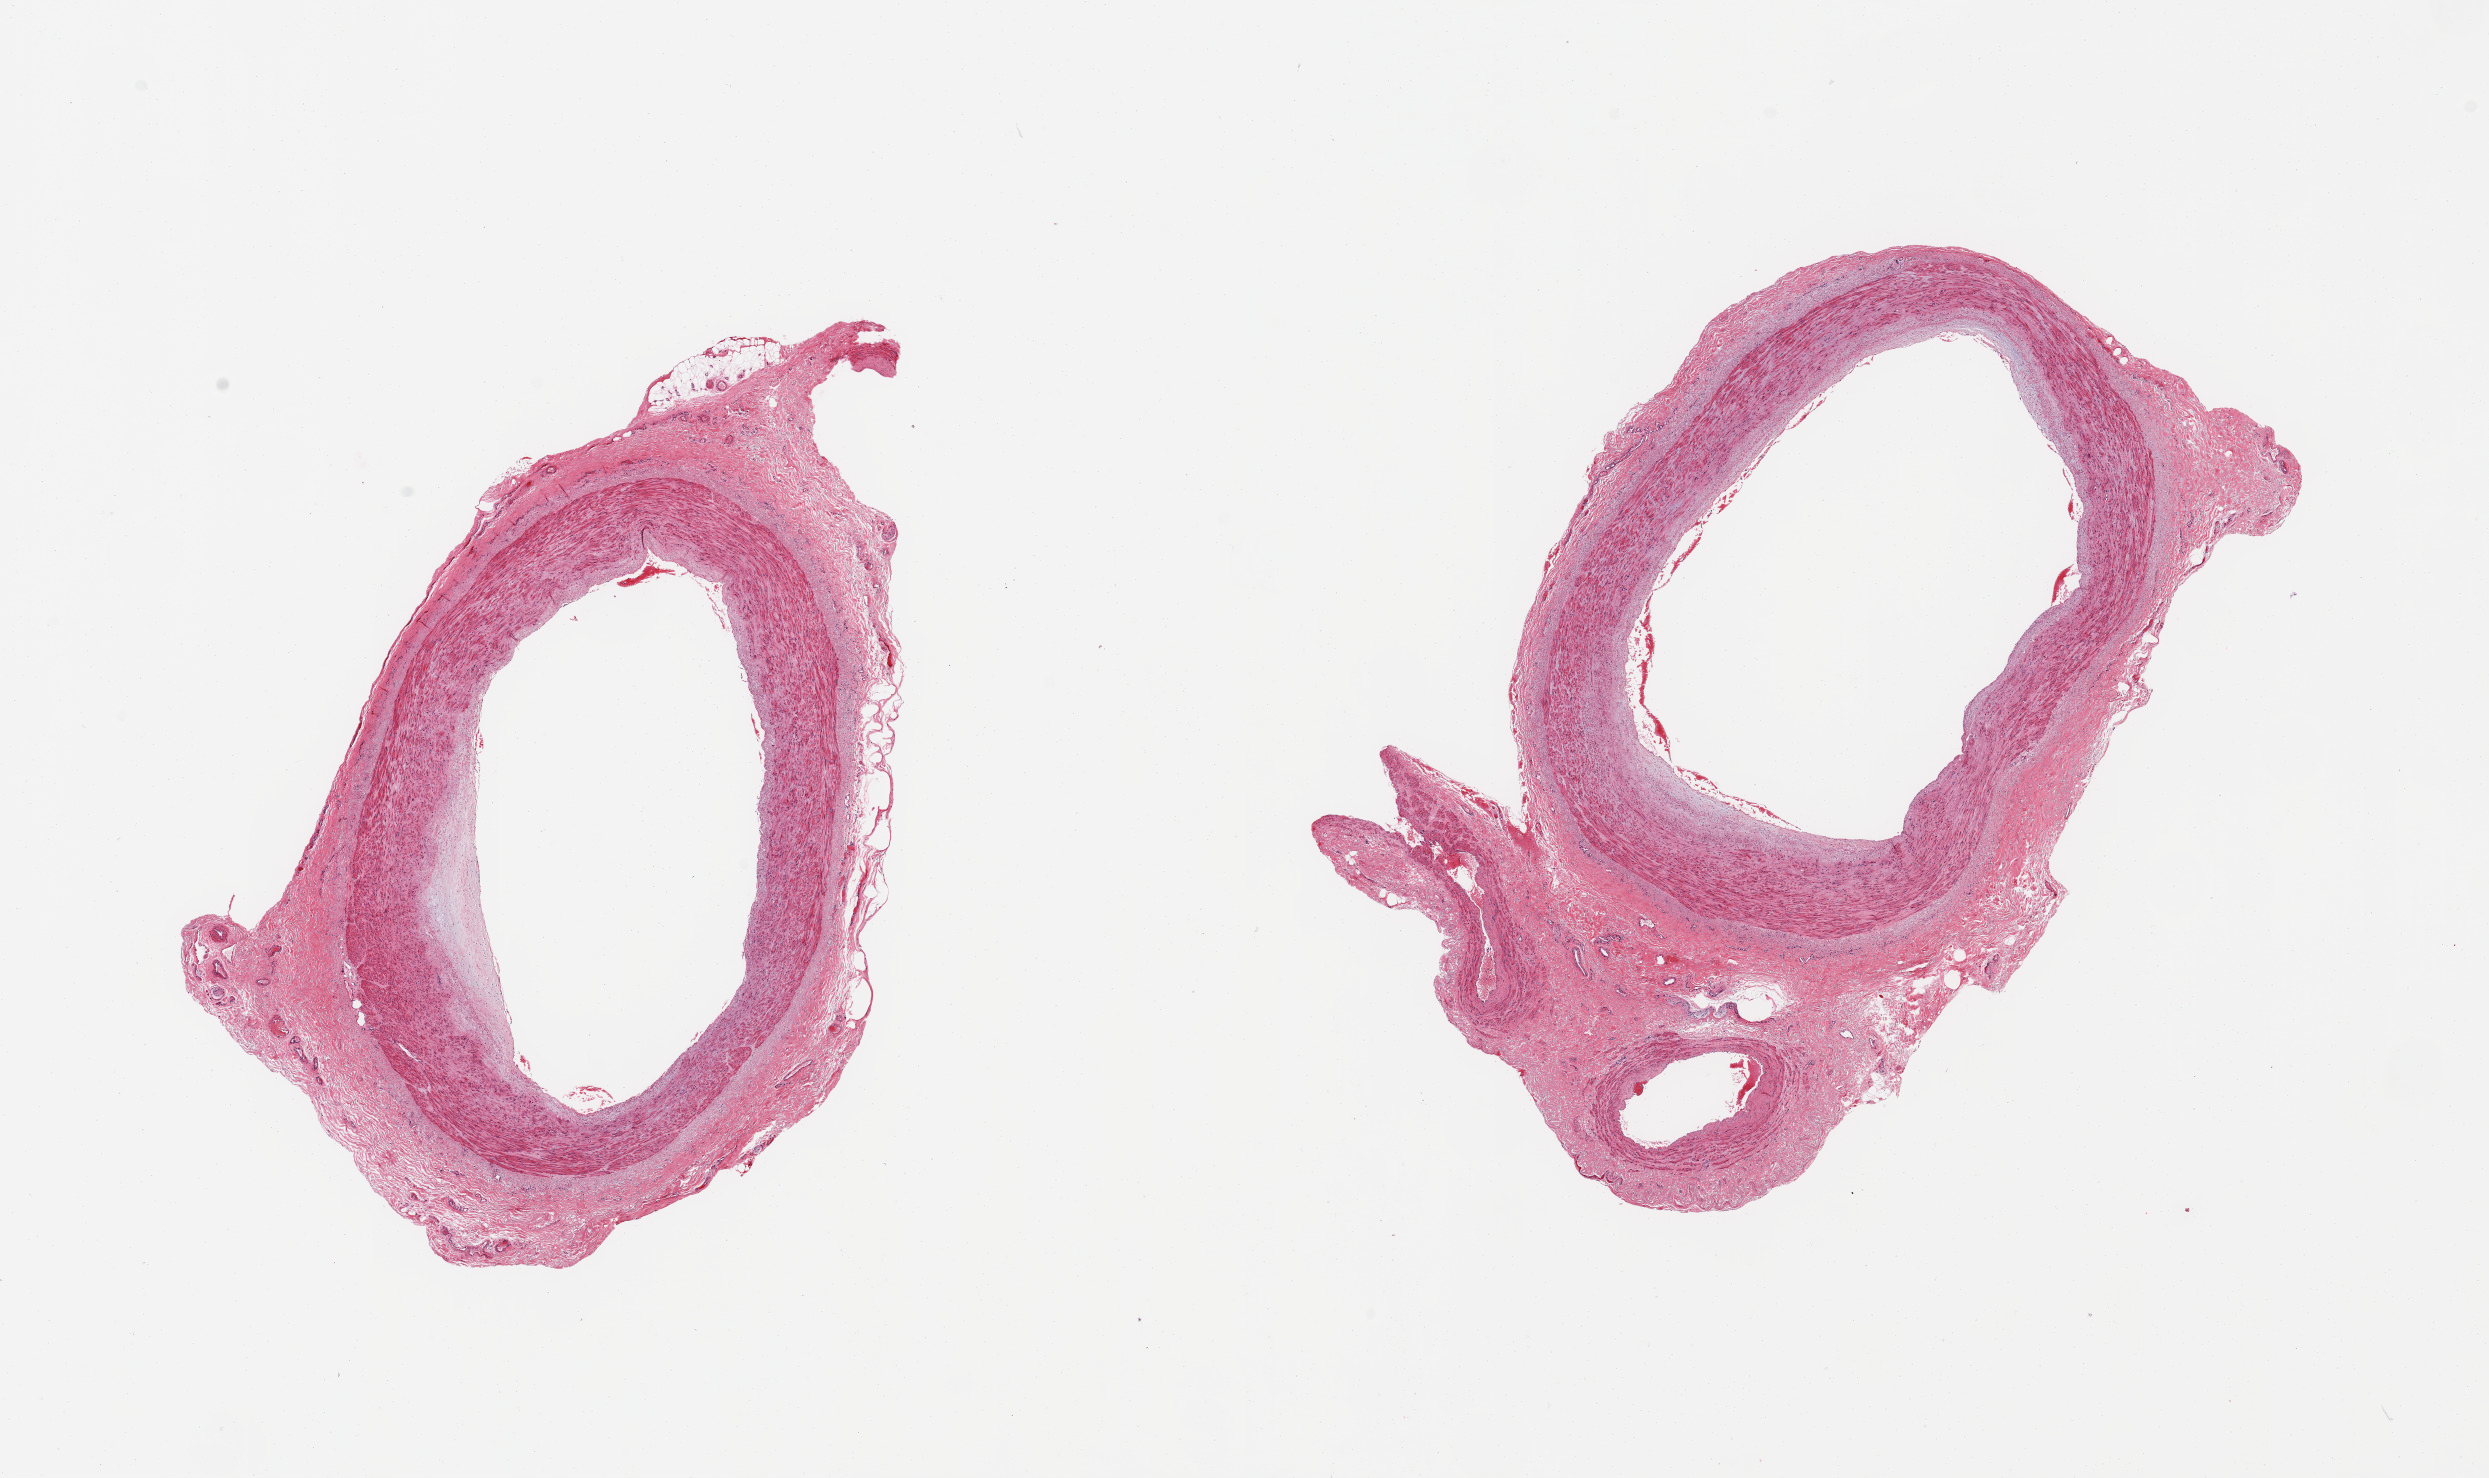
Whole-slide image, haematoxylin and eosin stain, brightfield, low-resolution overview of the scanned area, about 19.7 x 11.7 mm (slide scanned at 20x), PAXgene-fixed, paraffin-embedded tissue, target tissue: tibial artery, donor tissue sample. Donor sex: male.
Reviewer comment on this tissue sample: 2 pieces; small attachment of fat/vessels, mild, eccentric plaque.